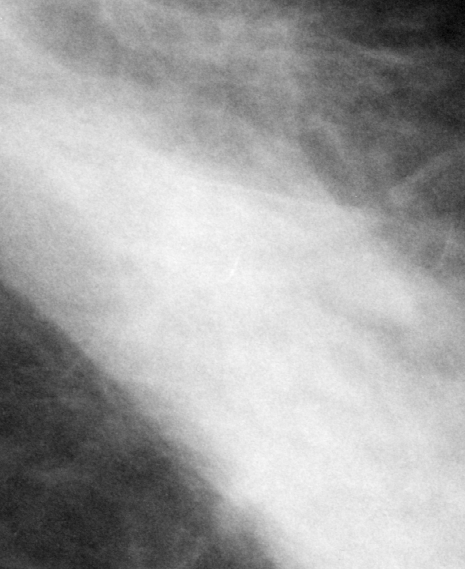
Region of interest cut from a scanned film mammogram (one marked finding), left breast, CC view, BI-RADS breast density category 2 (scale 1–4).
Marked abnormality: calcifications, morphology fine linear branching, distribution linear; BI-RADS assessment category 4; pathology (as recorded): benign.